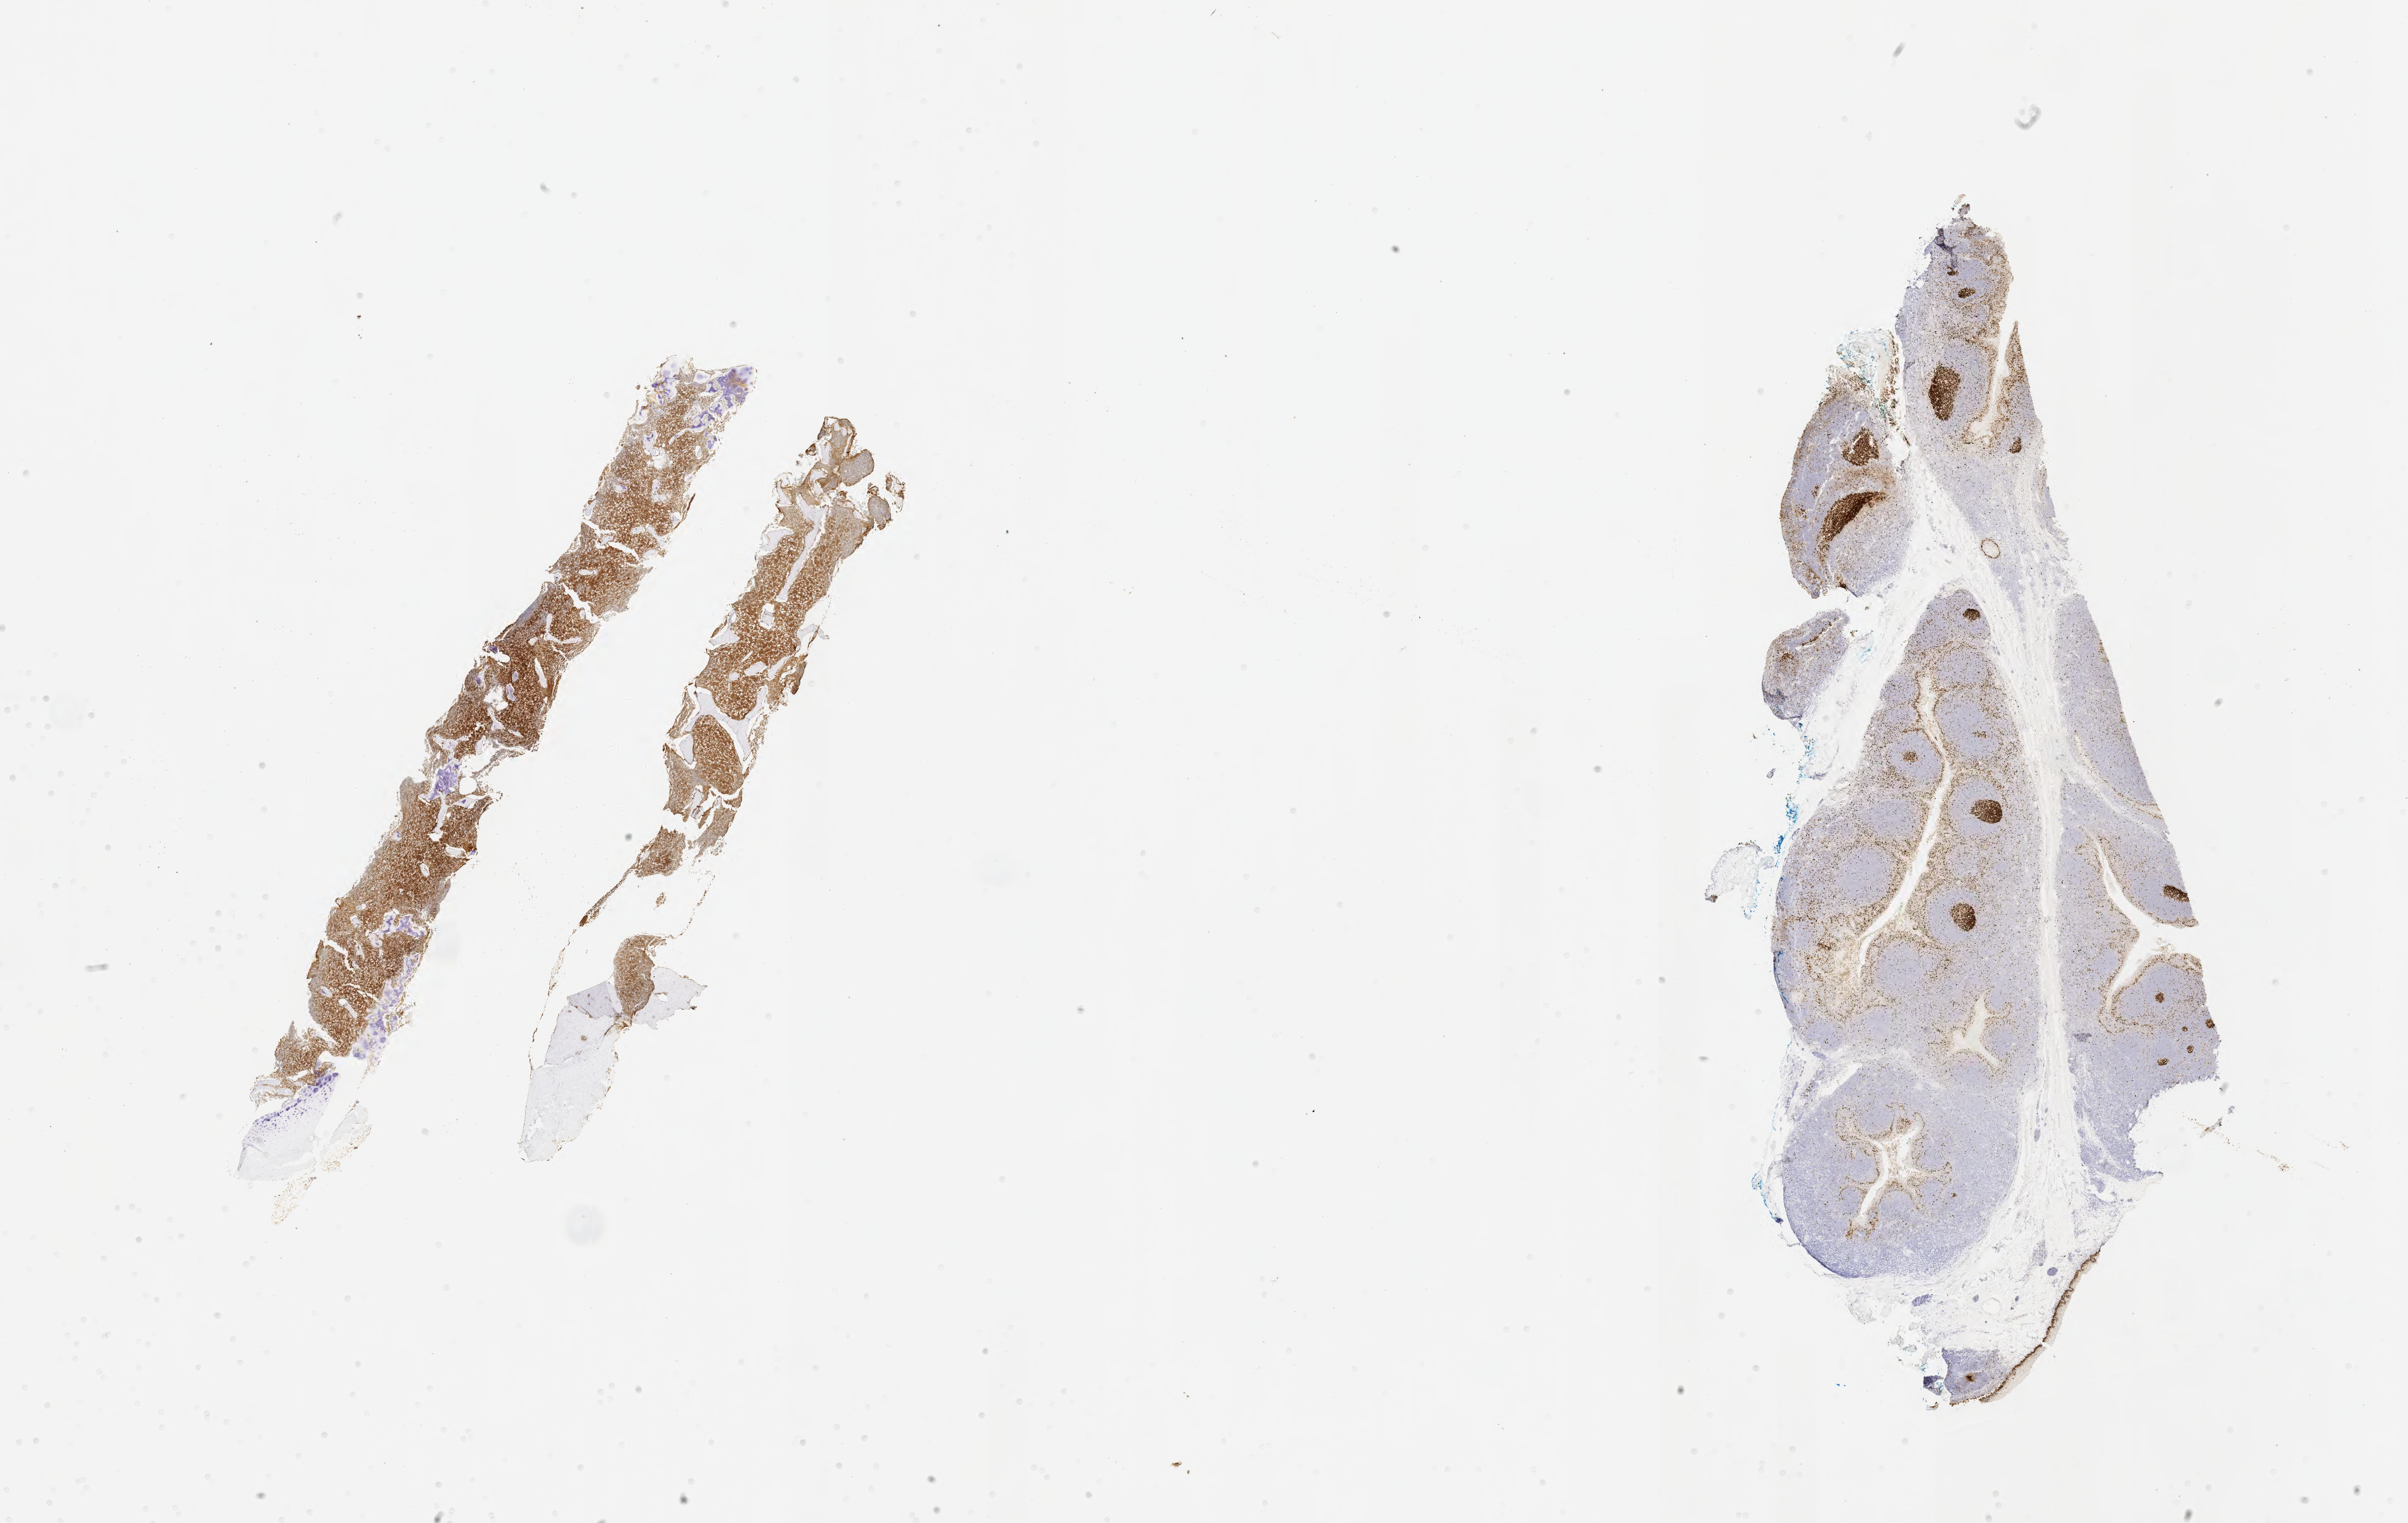
Immunohistochemistry (IHC) whole-slide image stained for Ki-67, whole scanned area (about 30.7 x 19.4 mm) shown as a low-resolution overview. Specimen: tumor tissue. Site: bone marrow. Patient: male, 16 years old.
Diagnosis: Burkitt lymphoma, NOS.